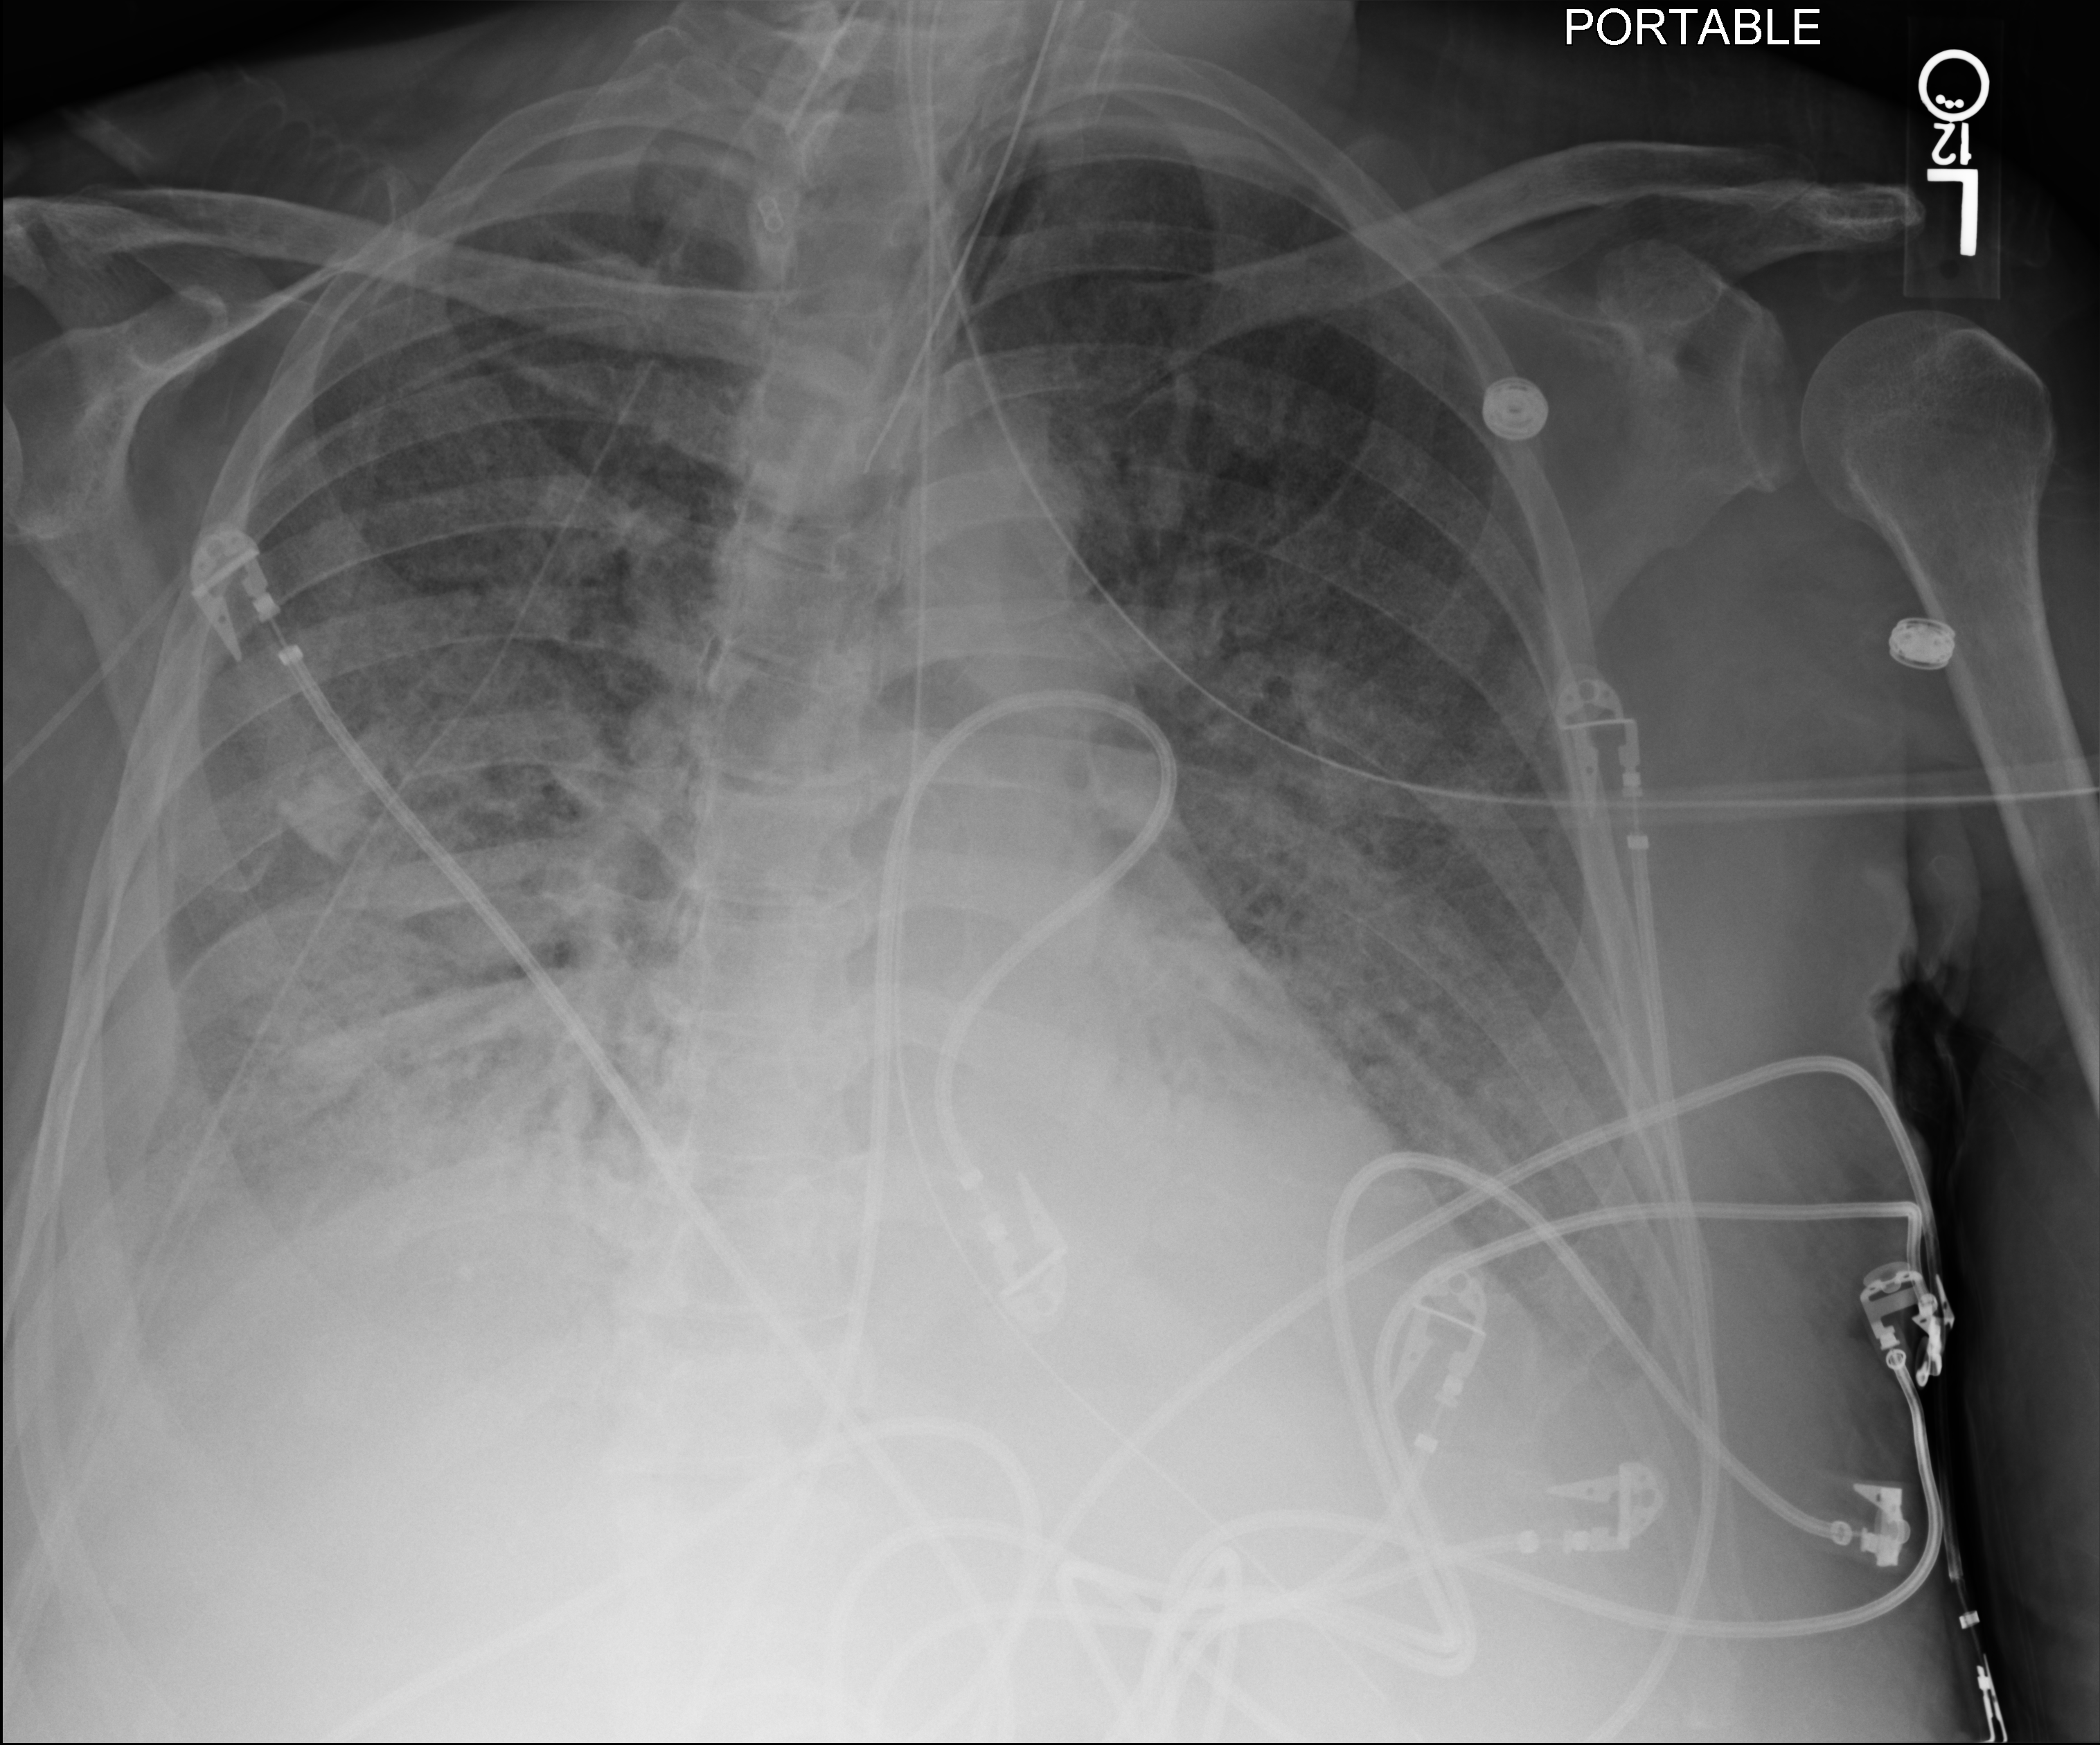
Portable chest radiograph, anteroposterior (AP) projection. Patient hospitalised with COVID-19; male, aged 60–74 years.
Hospital-stay facts (about this admission, not read from this image; timing relative to this image not recorded):
- mechanically ventilated during this hospital stay: yes
- admitted to intensive care during this hospital stay: yes